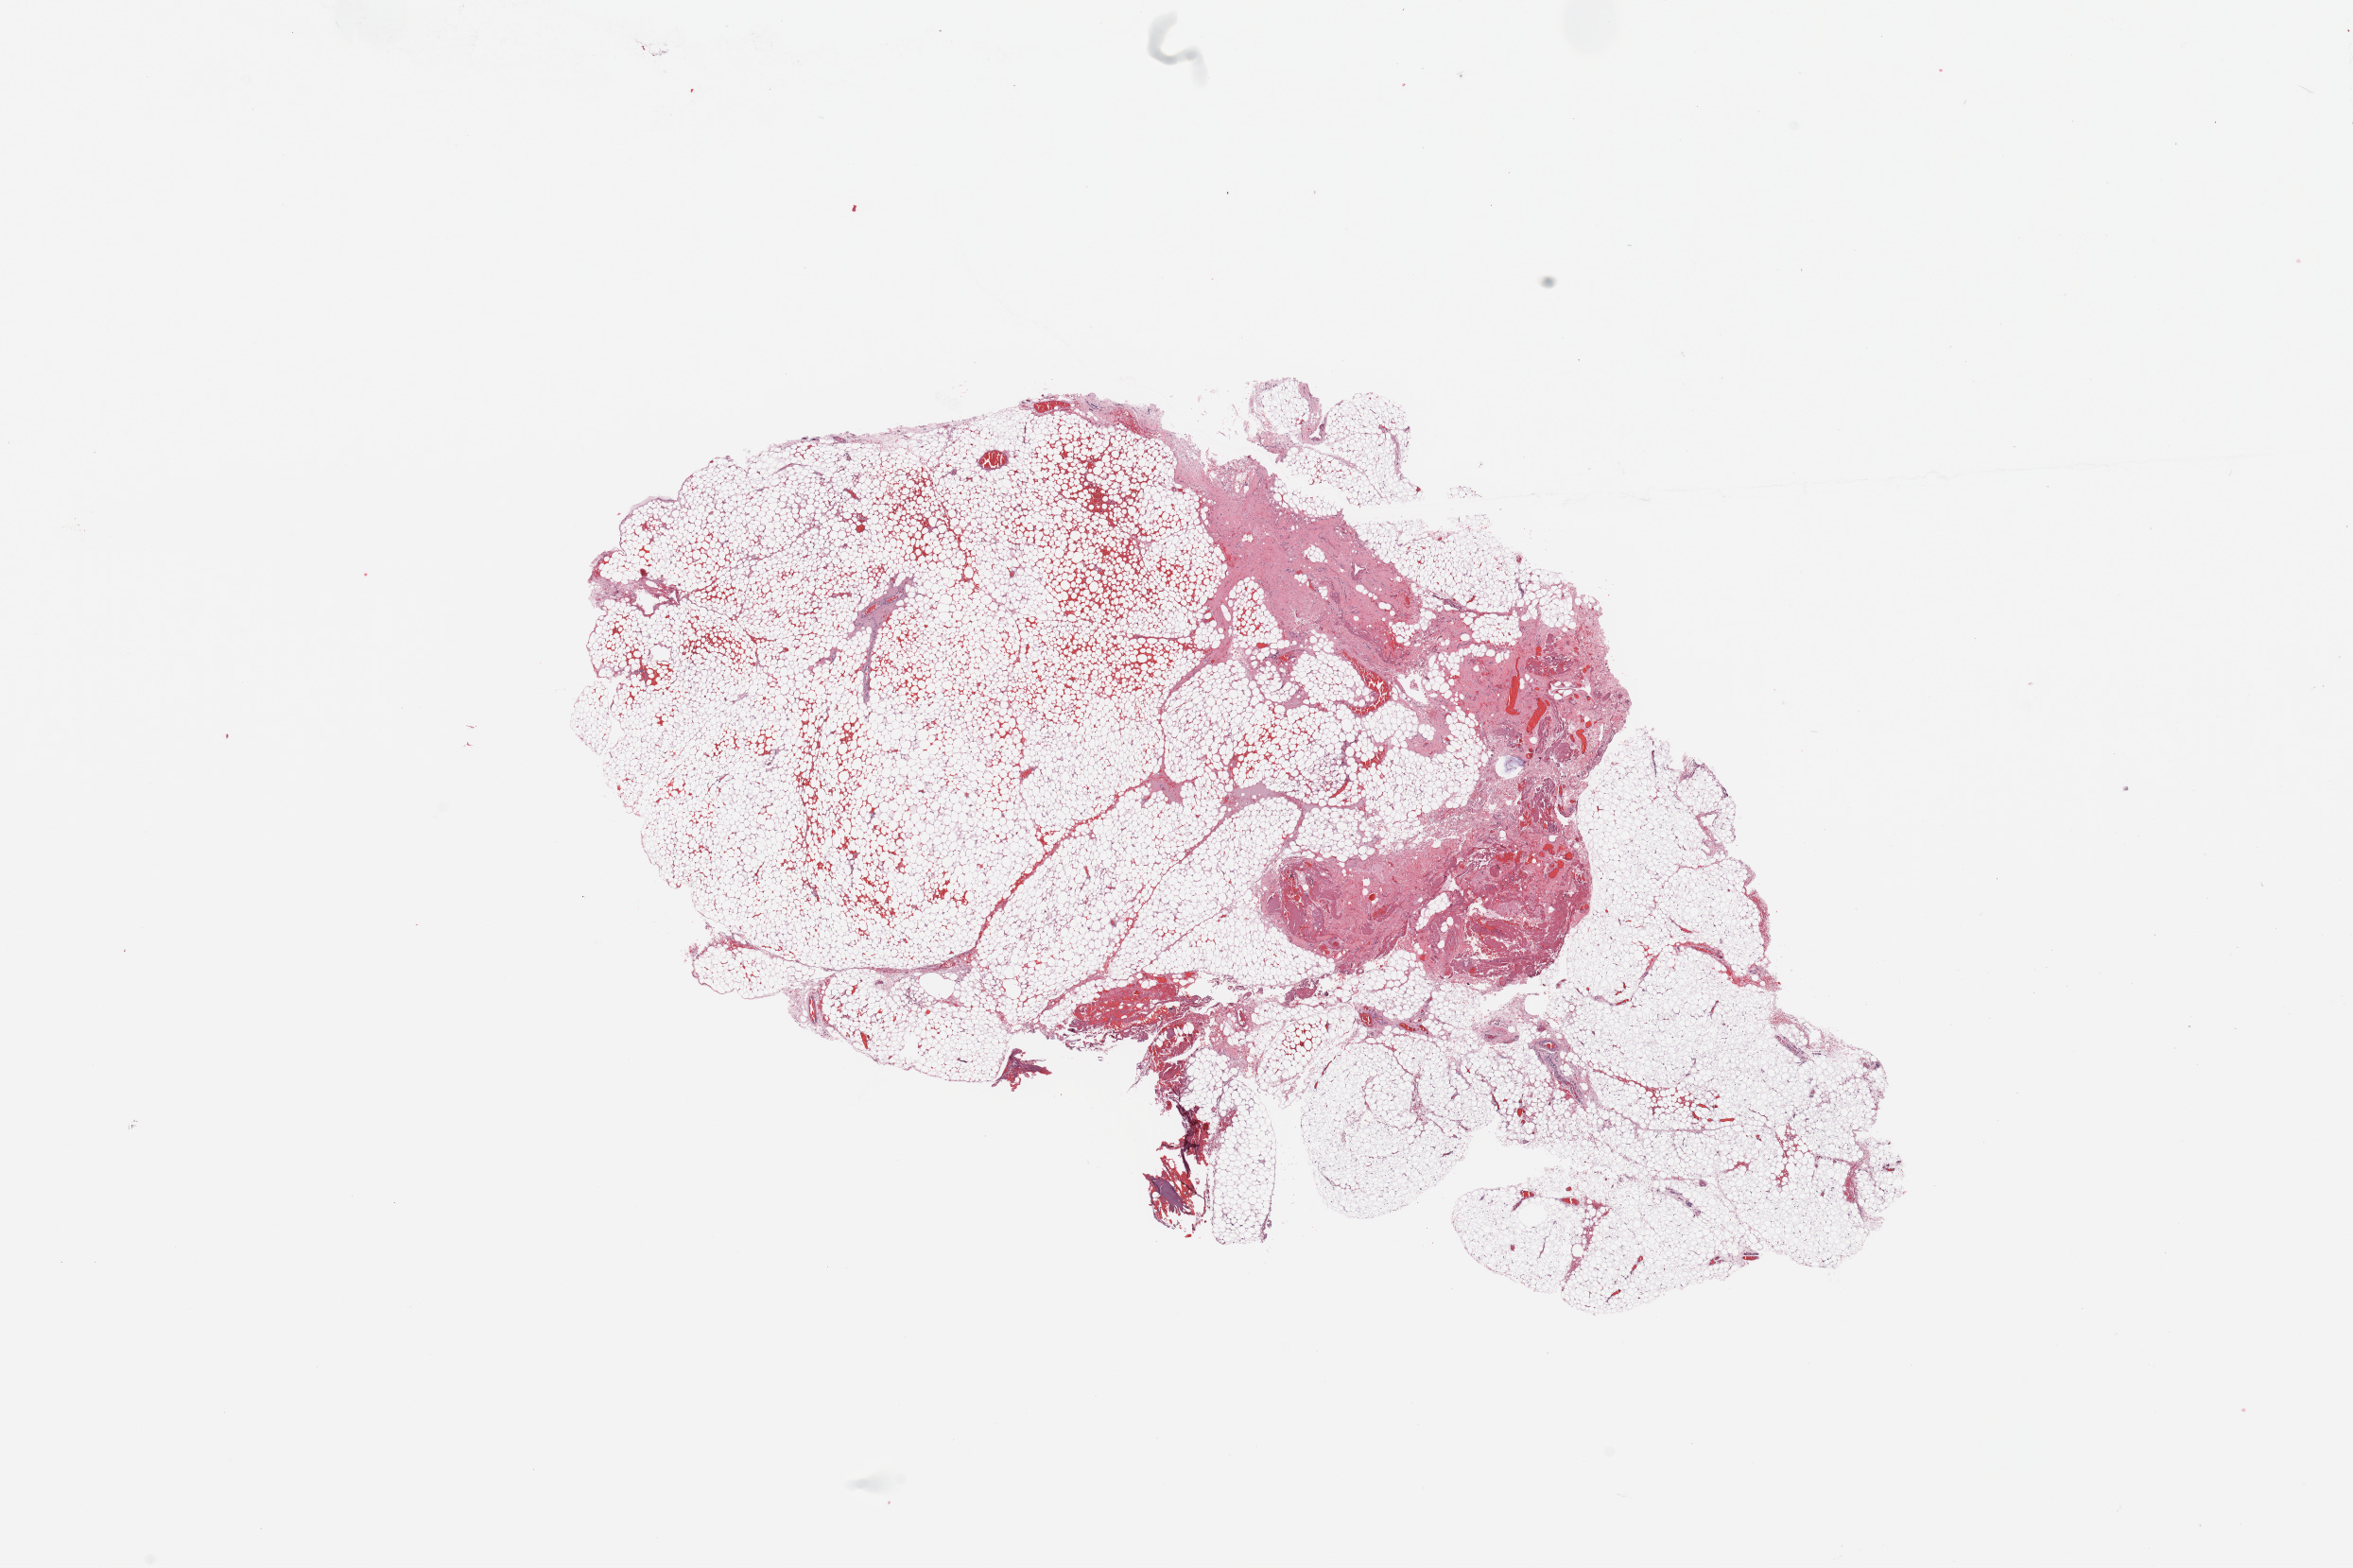
Digitized H&E-stained tissue section (whole slide), whole scanned area (about 19.7 x 13.1 mm) shown as a low-resolution overview, kidney, normal (non-tumour) tissue. 33-year-old male patient.
This section: normal (non-tumour) tissue from the same patient. Patient diagnosis: Renal cell carcinoma, NOS.